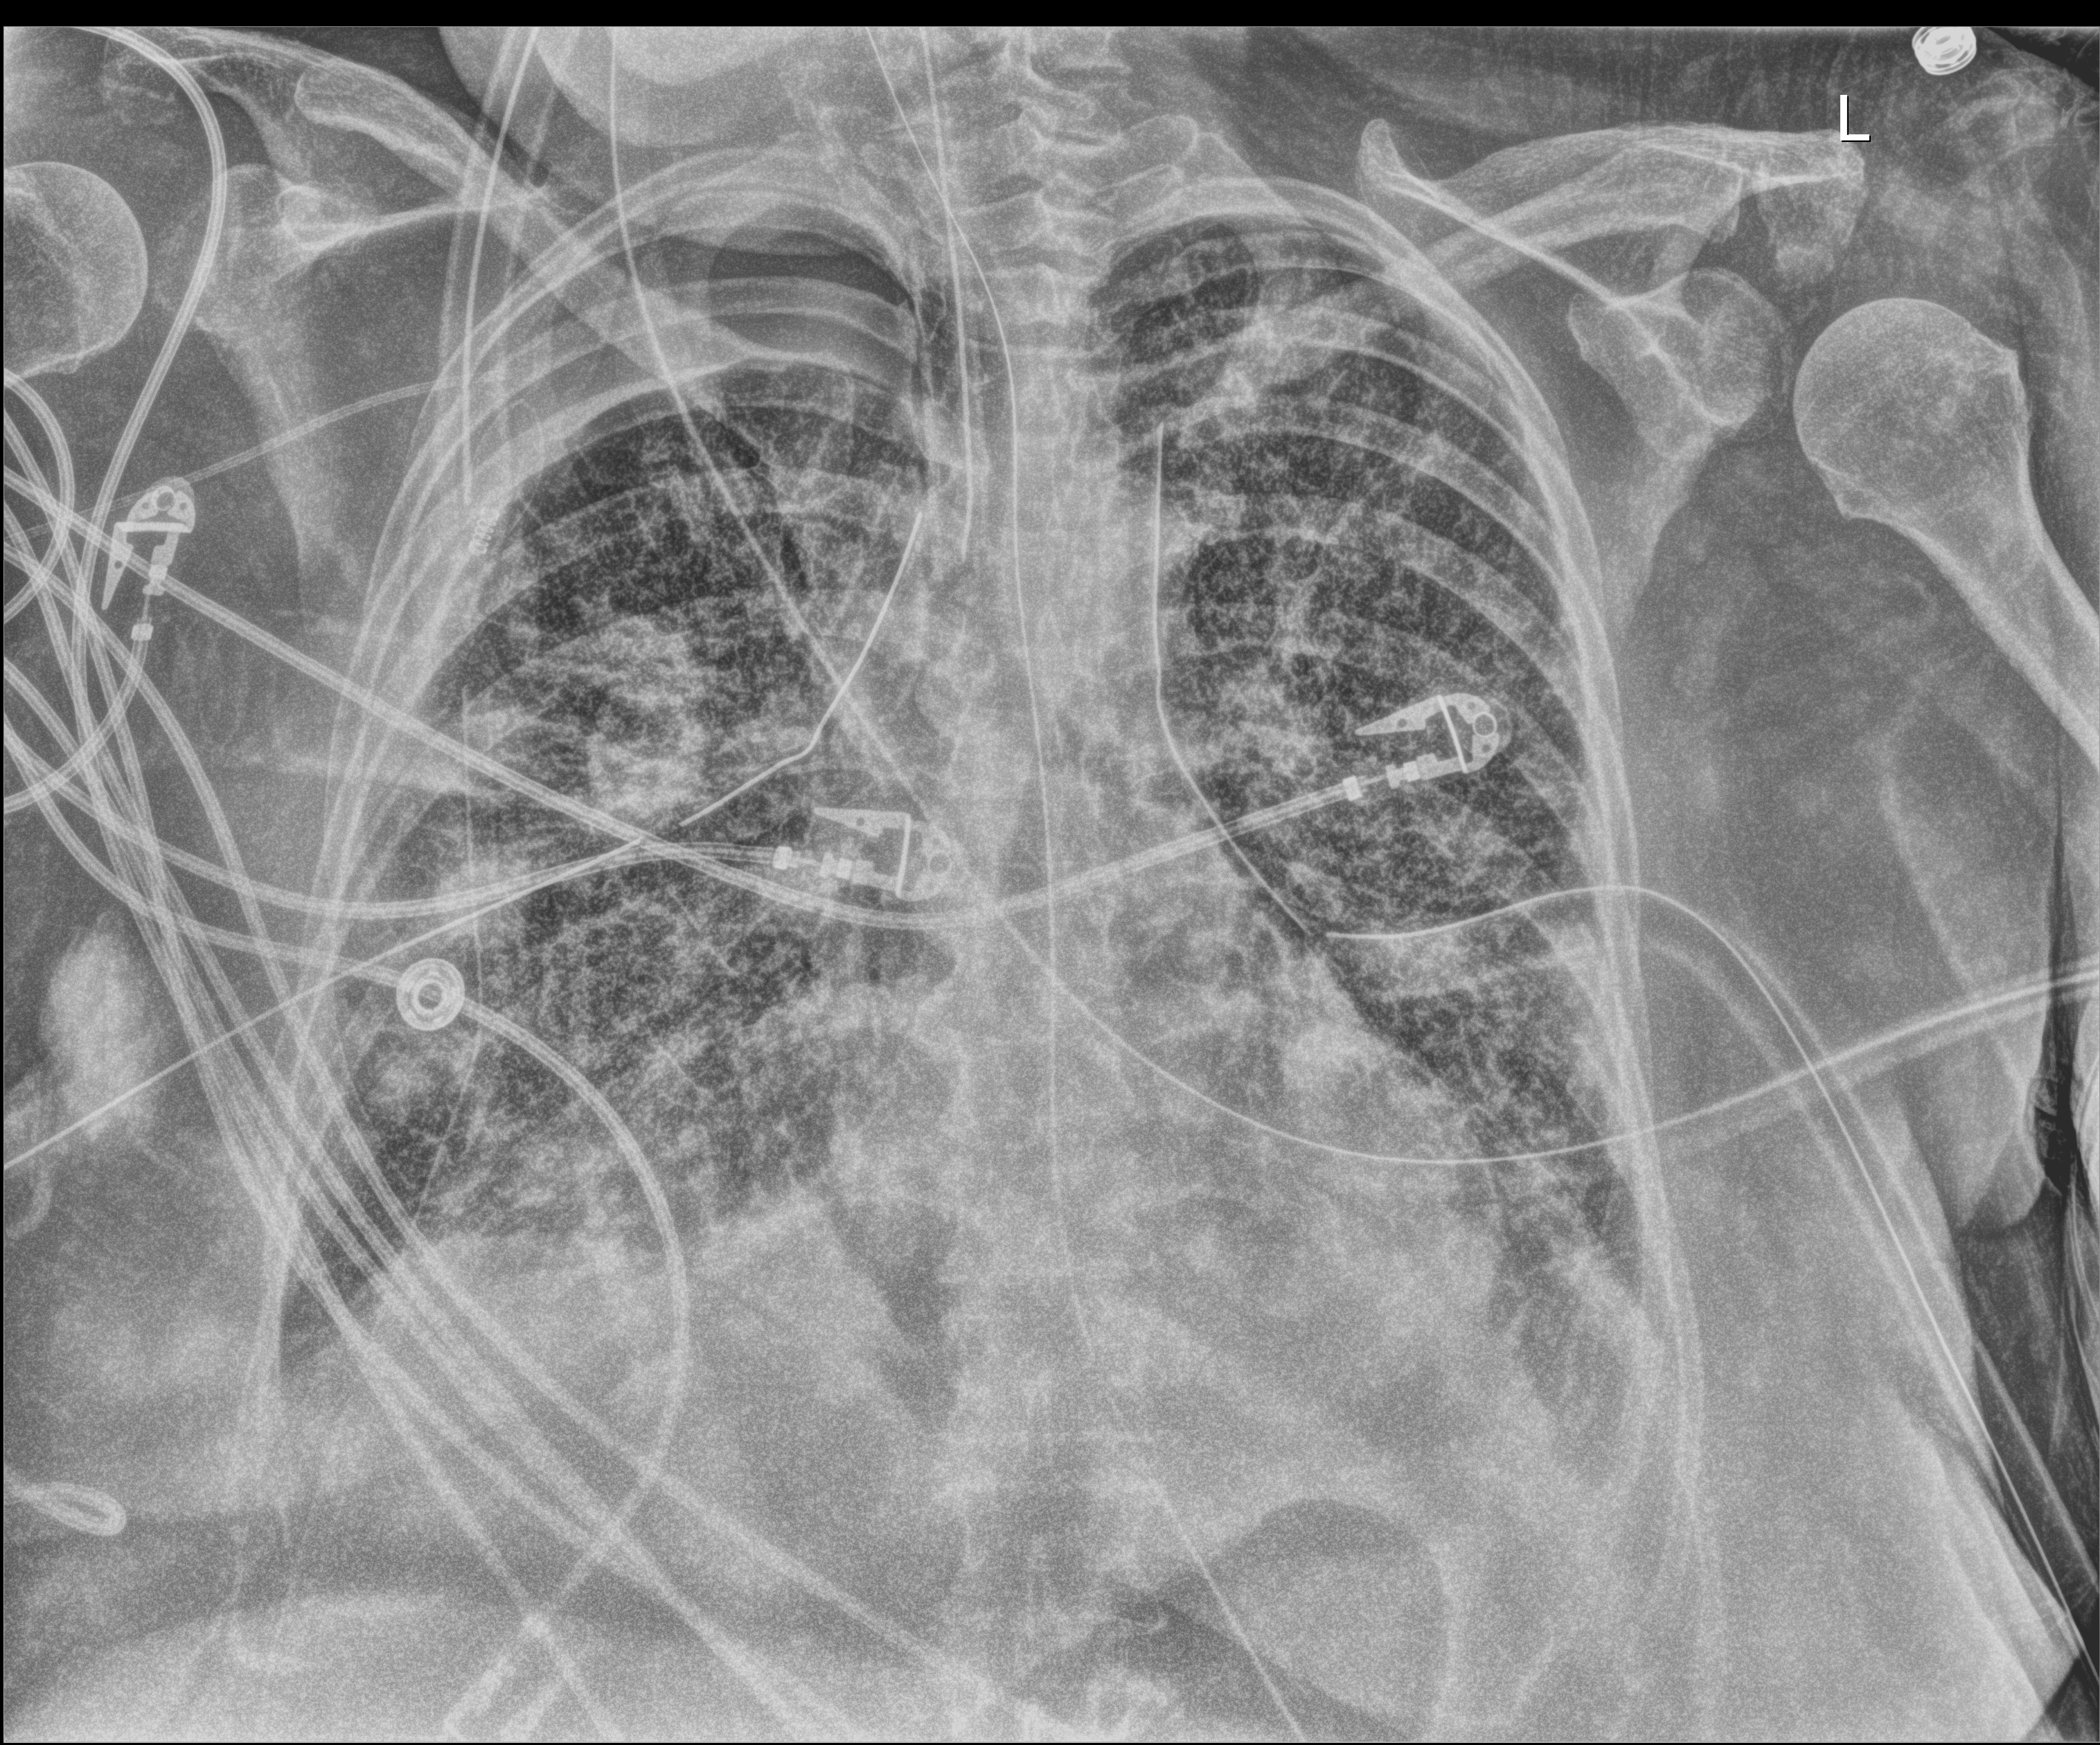
Bedside chest radiograph (digital radiography), anteroposterior (AP) projection. Female patient hospitalised with COVID-19, age 60–74 years.
From the hospital-stay record, not from the radiograph (when in the stay this image was taken is not recorded):
- mechanically ventilated during this hospital stay: yes
- admitted to intensive care during this hospital stay: yes